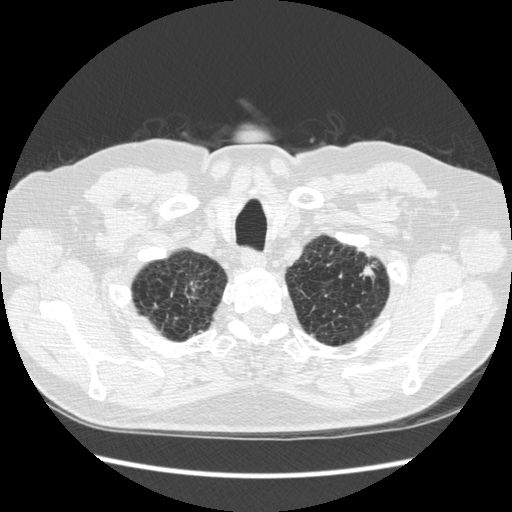
Low-dose screening chest CT, one axial slice. Position 244 of 267 along the scan axis. Reconstruction kernel STANDARD. 120 kVp. Lung window (W 1500 / L -600 HU). 512 × 512 image matrix, field of view 360 × 360 mm.
Structures marked on this image (manually delineated by an expert):
- lesion 1 (tumor, upper lobe of left lung): bounding box [x1, y1, x2, y2] px = [363, 266, 373, 276]